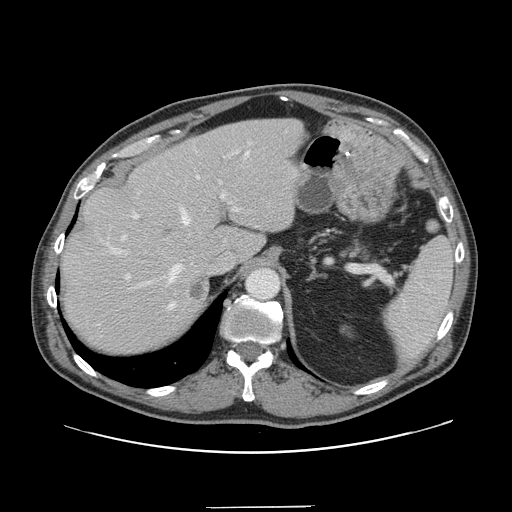
Contrast-enhanced abdominal CT, one axial slice. Slice 108 of 139 in the series (ordered by position). 120 kVp. Intravenous contrast given. Soft-tissue window (W 400 / L 40 HU). 512 × 512 image matrix, field of view 397 × 397 mm. Male patient, age 64 years. Case-level facts recorded for this patient, not image findings: diagnosis: colorectal cancer liver metastases, imaged before liver resection; multiple liver metastases: yes; largest metastasis: 3.5 cm; chemotherapy before resection: yes.
Structures marked on this image (outlined manually by an expert reader):
- hepatic veins: bounding box [x1, y1, x2, y2] px = [111, 152, 249, 309]
- liver: [62, 119, 302, 352]
- planned liver remnant (the part of the liver to remain after resection): [62, 120, 272, 352]
- portal vein (with intrahepatic branches): [121, 143, 250, 288]
- liver metastasis: [188, 277, 208, 302]